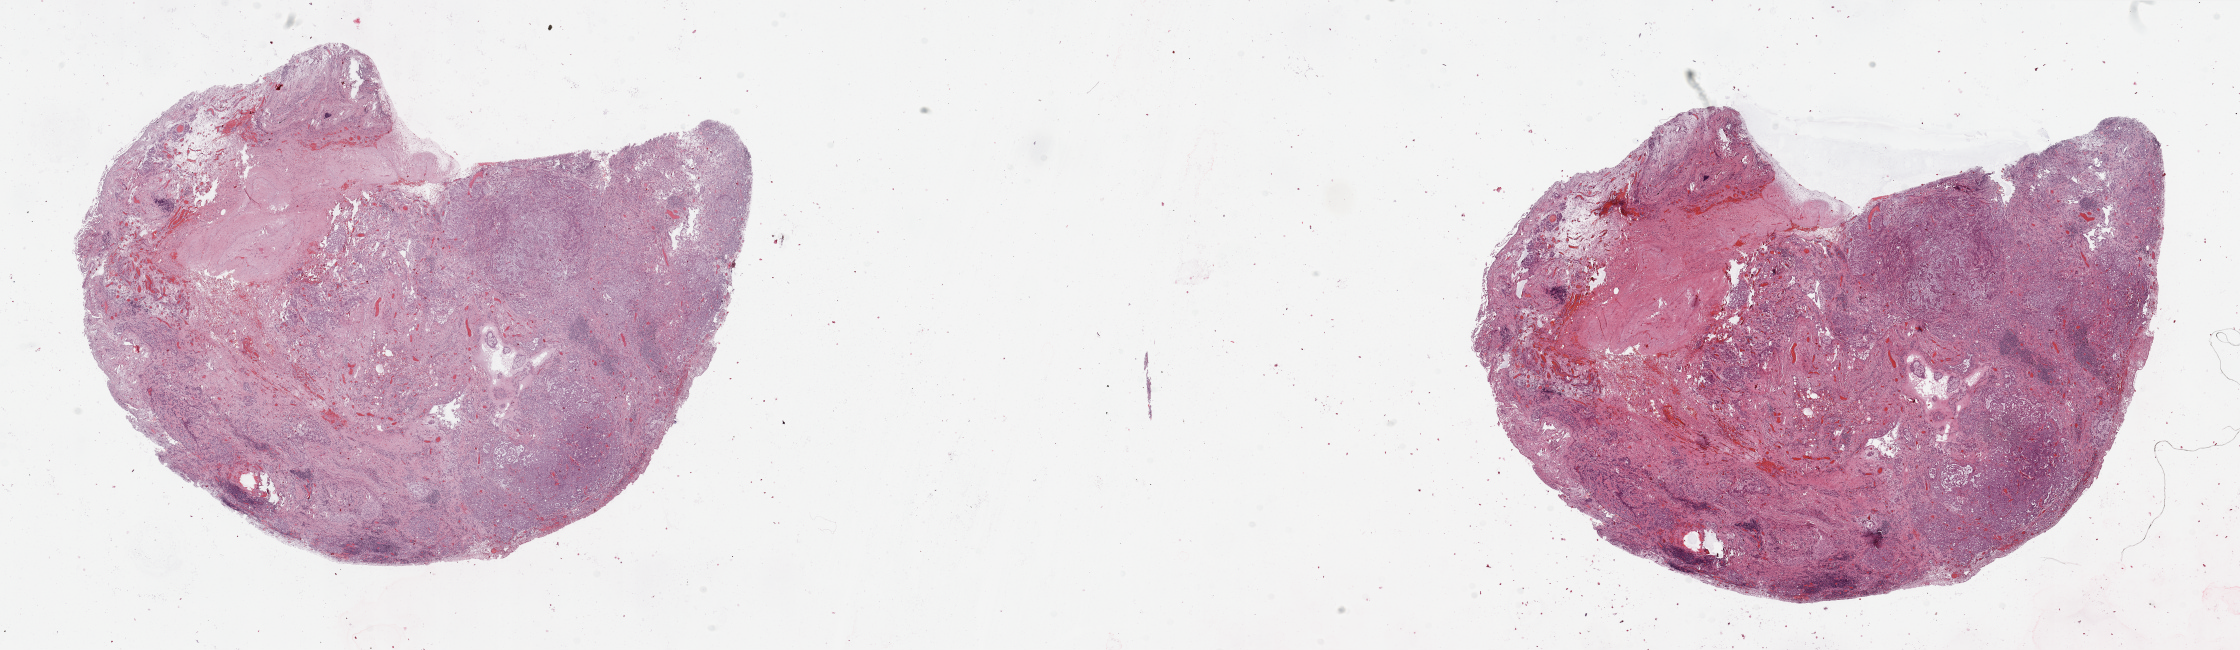
Digitized H&E-stained tissue section (whole slide), low-resolution overview of the scanned area, about 35.4 x 10.3 mm (from a 20x scan). Normal (non-tumour) tissue sample, lung. 73-year-old male patient.
This section: normal (non-tumour) tissue from the same patient. Patient diagnosis: Squamous cell carcinoma, NOS.